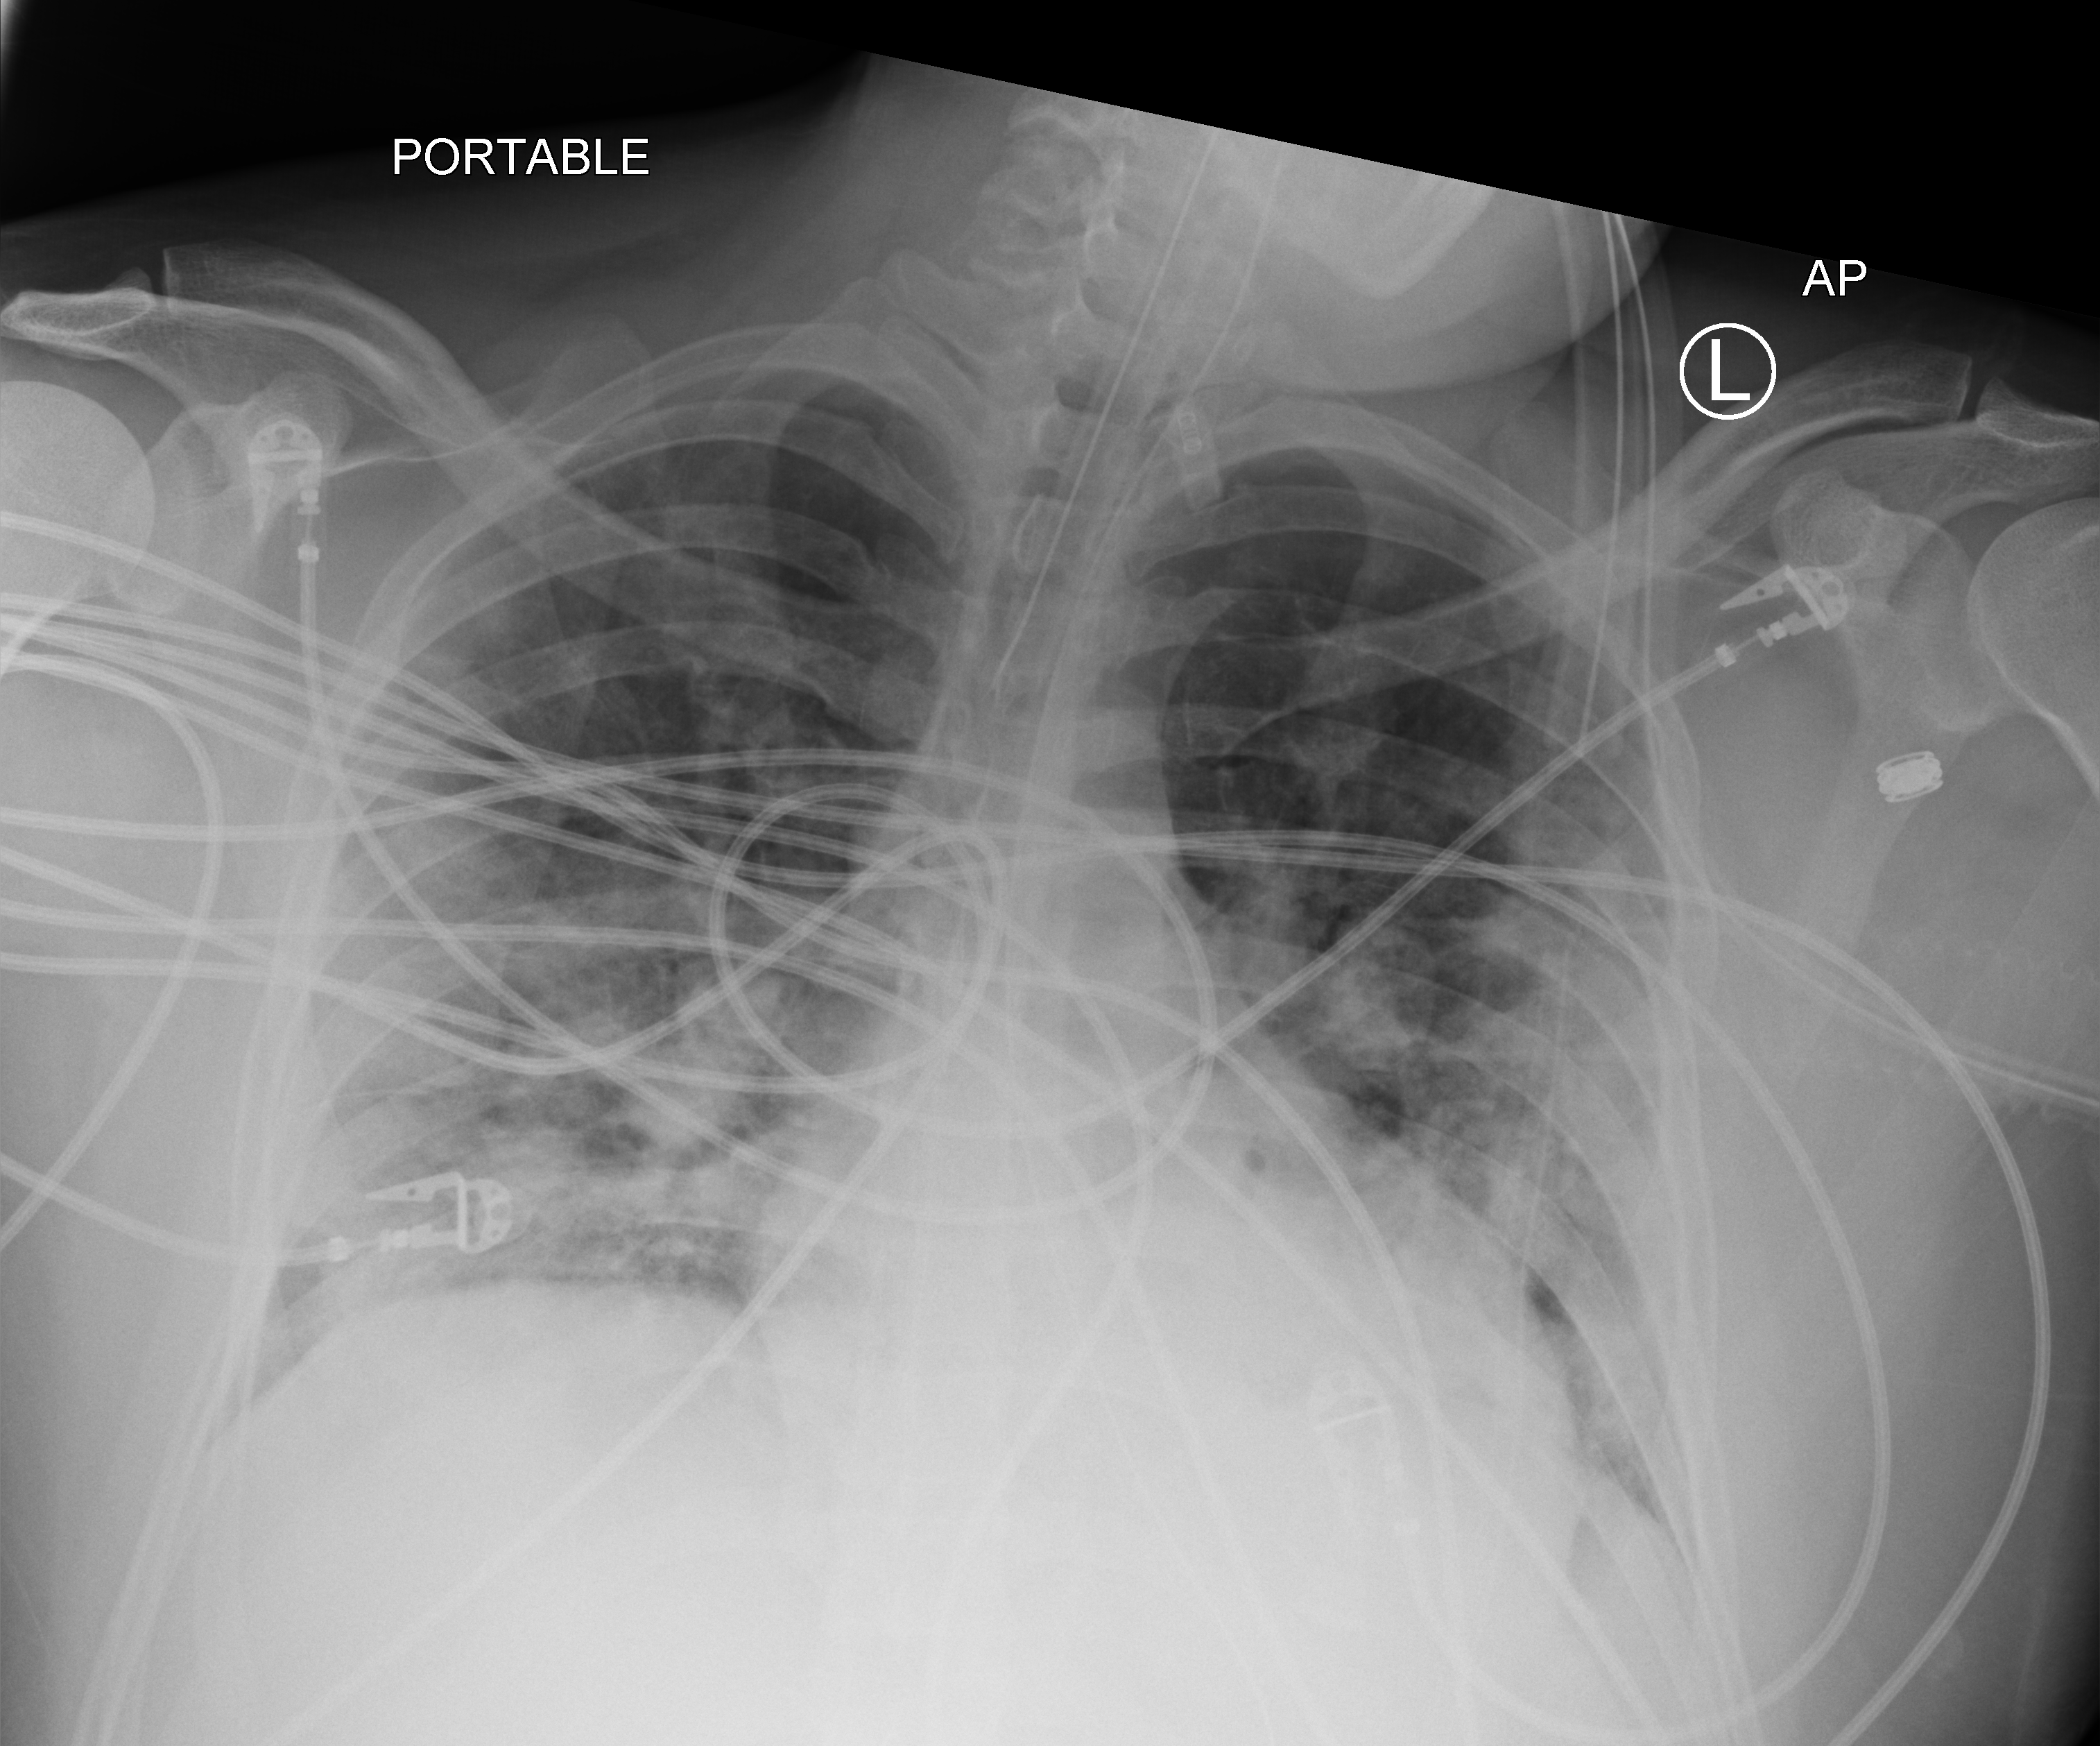
Chest X-ray (portable), anteroposterior (AP) projection. Patient hospitalised with COVID-19; male, aged 18–59 years.
From the hospital-stay record, not from the radiograph (when in the stay this image was taken is not recorded):
- mechanically ventilated during this hospital stay: yes
- admitted to intensive care during this hospital stay: yes
- other chronic lung disease (admission record): no